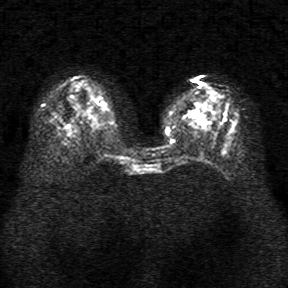
Breast MRI, one axial slice. Slice 14 of 34 in the series (ordered by position). Diffusion-weighted series; image 2 of 4 stored at this slice position (different b-values; order by instance number). 1.5 T. 288 × 288 image matrix. Female patient.
Annotated regions visible in this slice (expert manual segmentation):
- tumour on diffusion-weighted imaging: bounding box [x1, y1, x2, y2] px = [197, 115, 205, 123]